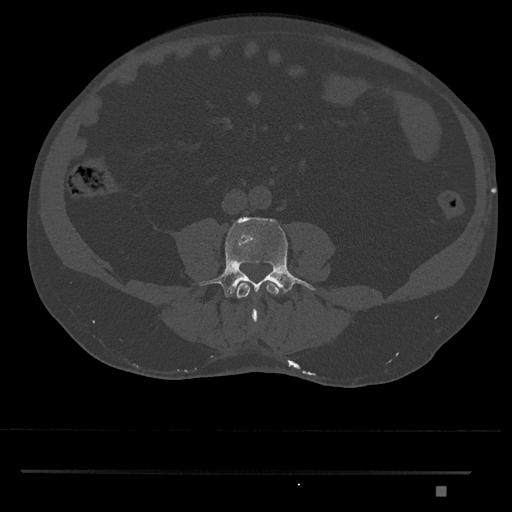
CT including the spine, one axial slice. Position 632 of 1134 along the scan axis. Reconstruction kernel Br40s/3. 120 kVp. Bone window (W 1800 / L 400 HU). 0.5 mm slice thickness. 512 × 512 image matrix, field of view 429 × 429 mm. Male patient, age 65 years. Case-level facts recorded for this patient, not image findings: primary cancer: prostate.
Outlined on this slice (semi-automatically segmented with operator editing):
- L3 vertebra: bounding box <236,282,279,322> (left, top, right, bottom; pixels)
- L4 vertebra: <200,217,314,318>